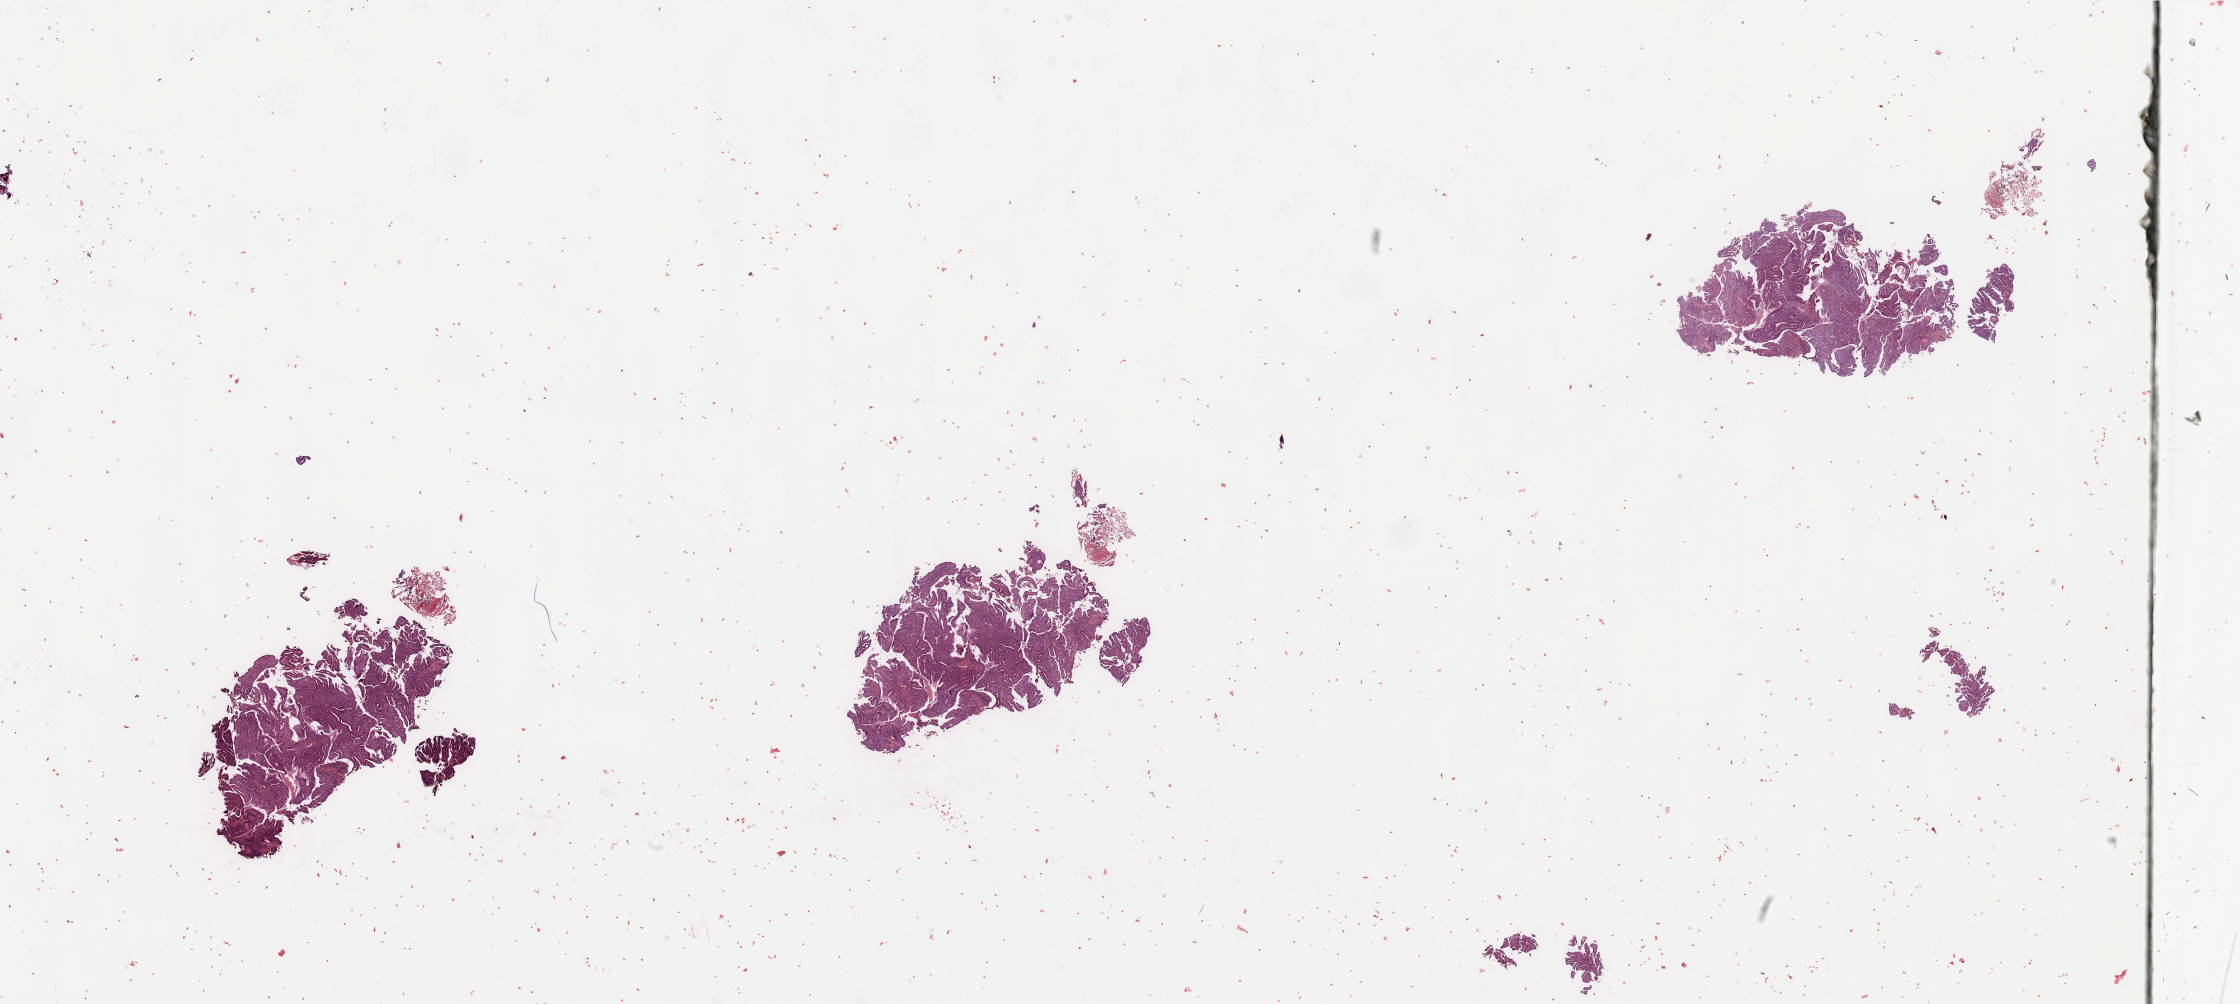
Digitized H&E-stained tissue section (whole slide), whole scanned area (about 35.4 x 15.9 mm) shown as a low-resolution overview. Uterus, tumour tissue. Patient: female, age 58 years. Histologic grade: G2 (moderately differentiated).
- primary tumour site (as recorded): anterior endometrium
- diagnosis: Endometrioid adenocarcinoma, NOS
- AJCC pathologic stage: III